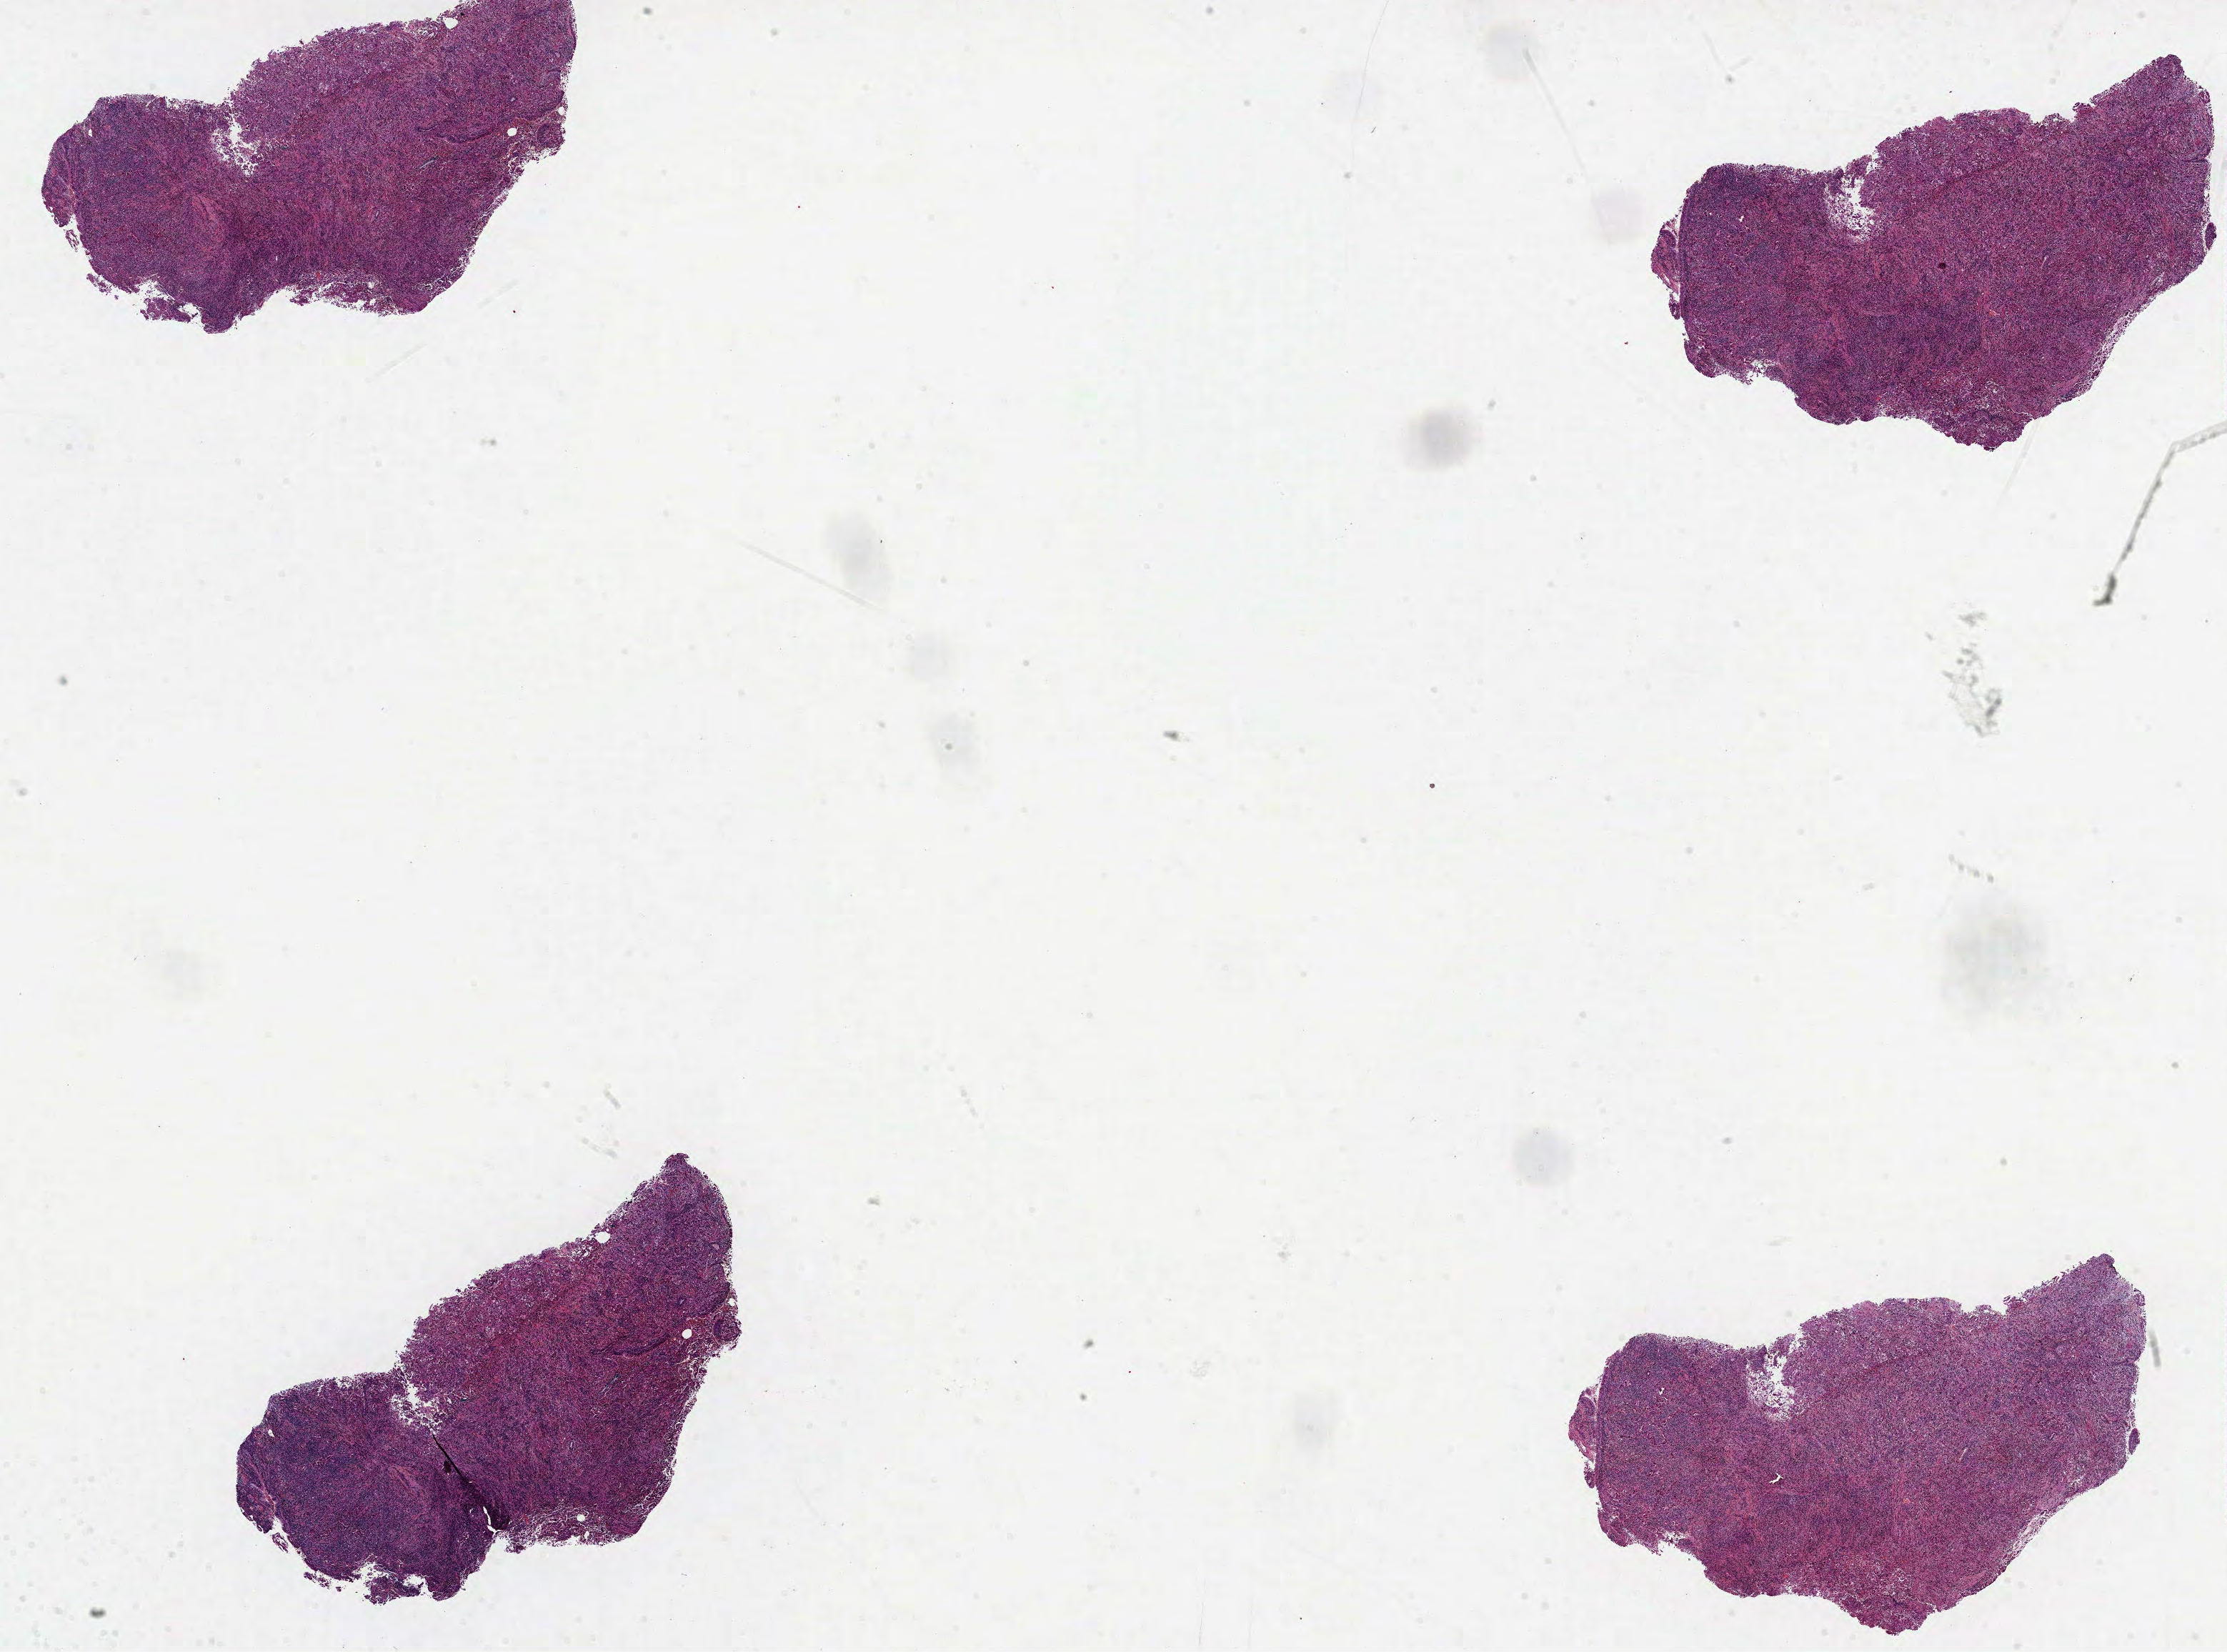
Digitized Hematoxylin and eosin (H&E) stained tissue section (whole slide) — shown as a low-resolution overview of the whole scanned area (about 25.1 x 18.6 mm), FFPE section, lung, primary tumour sample. Female patient; age at initial diagnosis 66 years.
- AJCC pathologic stage: IA (6th edition)
- diagnosis: Adenocarcinoma, NOS (lower lobe, lung)